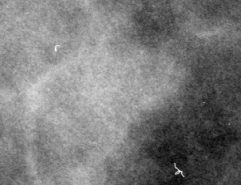
Cropped region of a digitized screen-film mammogram centred on a radiologist-marked abnormality; left breast; CC view; BI-RADS breast density category 3 (scale 1–4).
Marked abnormality: calcifications, morphology punctate / amorphous, distribution clustered / linear; BI-RADS assessment category 4; pathology result (as recorded, not read from the image): benign.